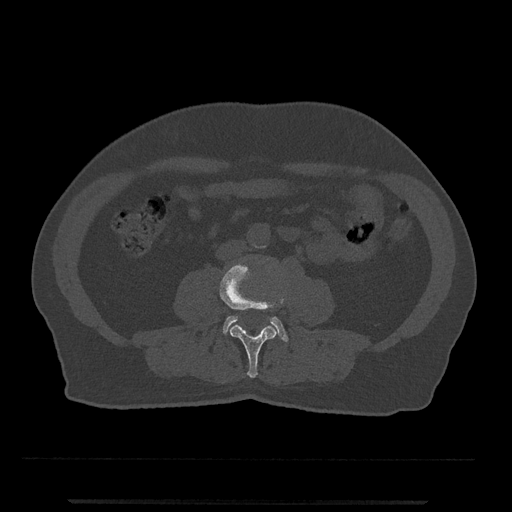
CT including the spine, one axial slice. Position 179 of 797 along the scan axis. Bone window (W 1800 / L 400 HU). 0.5 mm slice thickness. 512 × 512 image matrix, field of view 419 × 419 mm. Male patient, age 63 years. From the clinical record (not read from this slice): primary cancer: prostate.
Structures marked on this image (semi-automatically segmented with operator editing):
- L3 vertebra: bounding box [x1, y1, x2, y2] px = [220, 262, 285, 378]
- L4 vertebra: [223, 316, 288, 341]